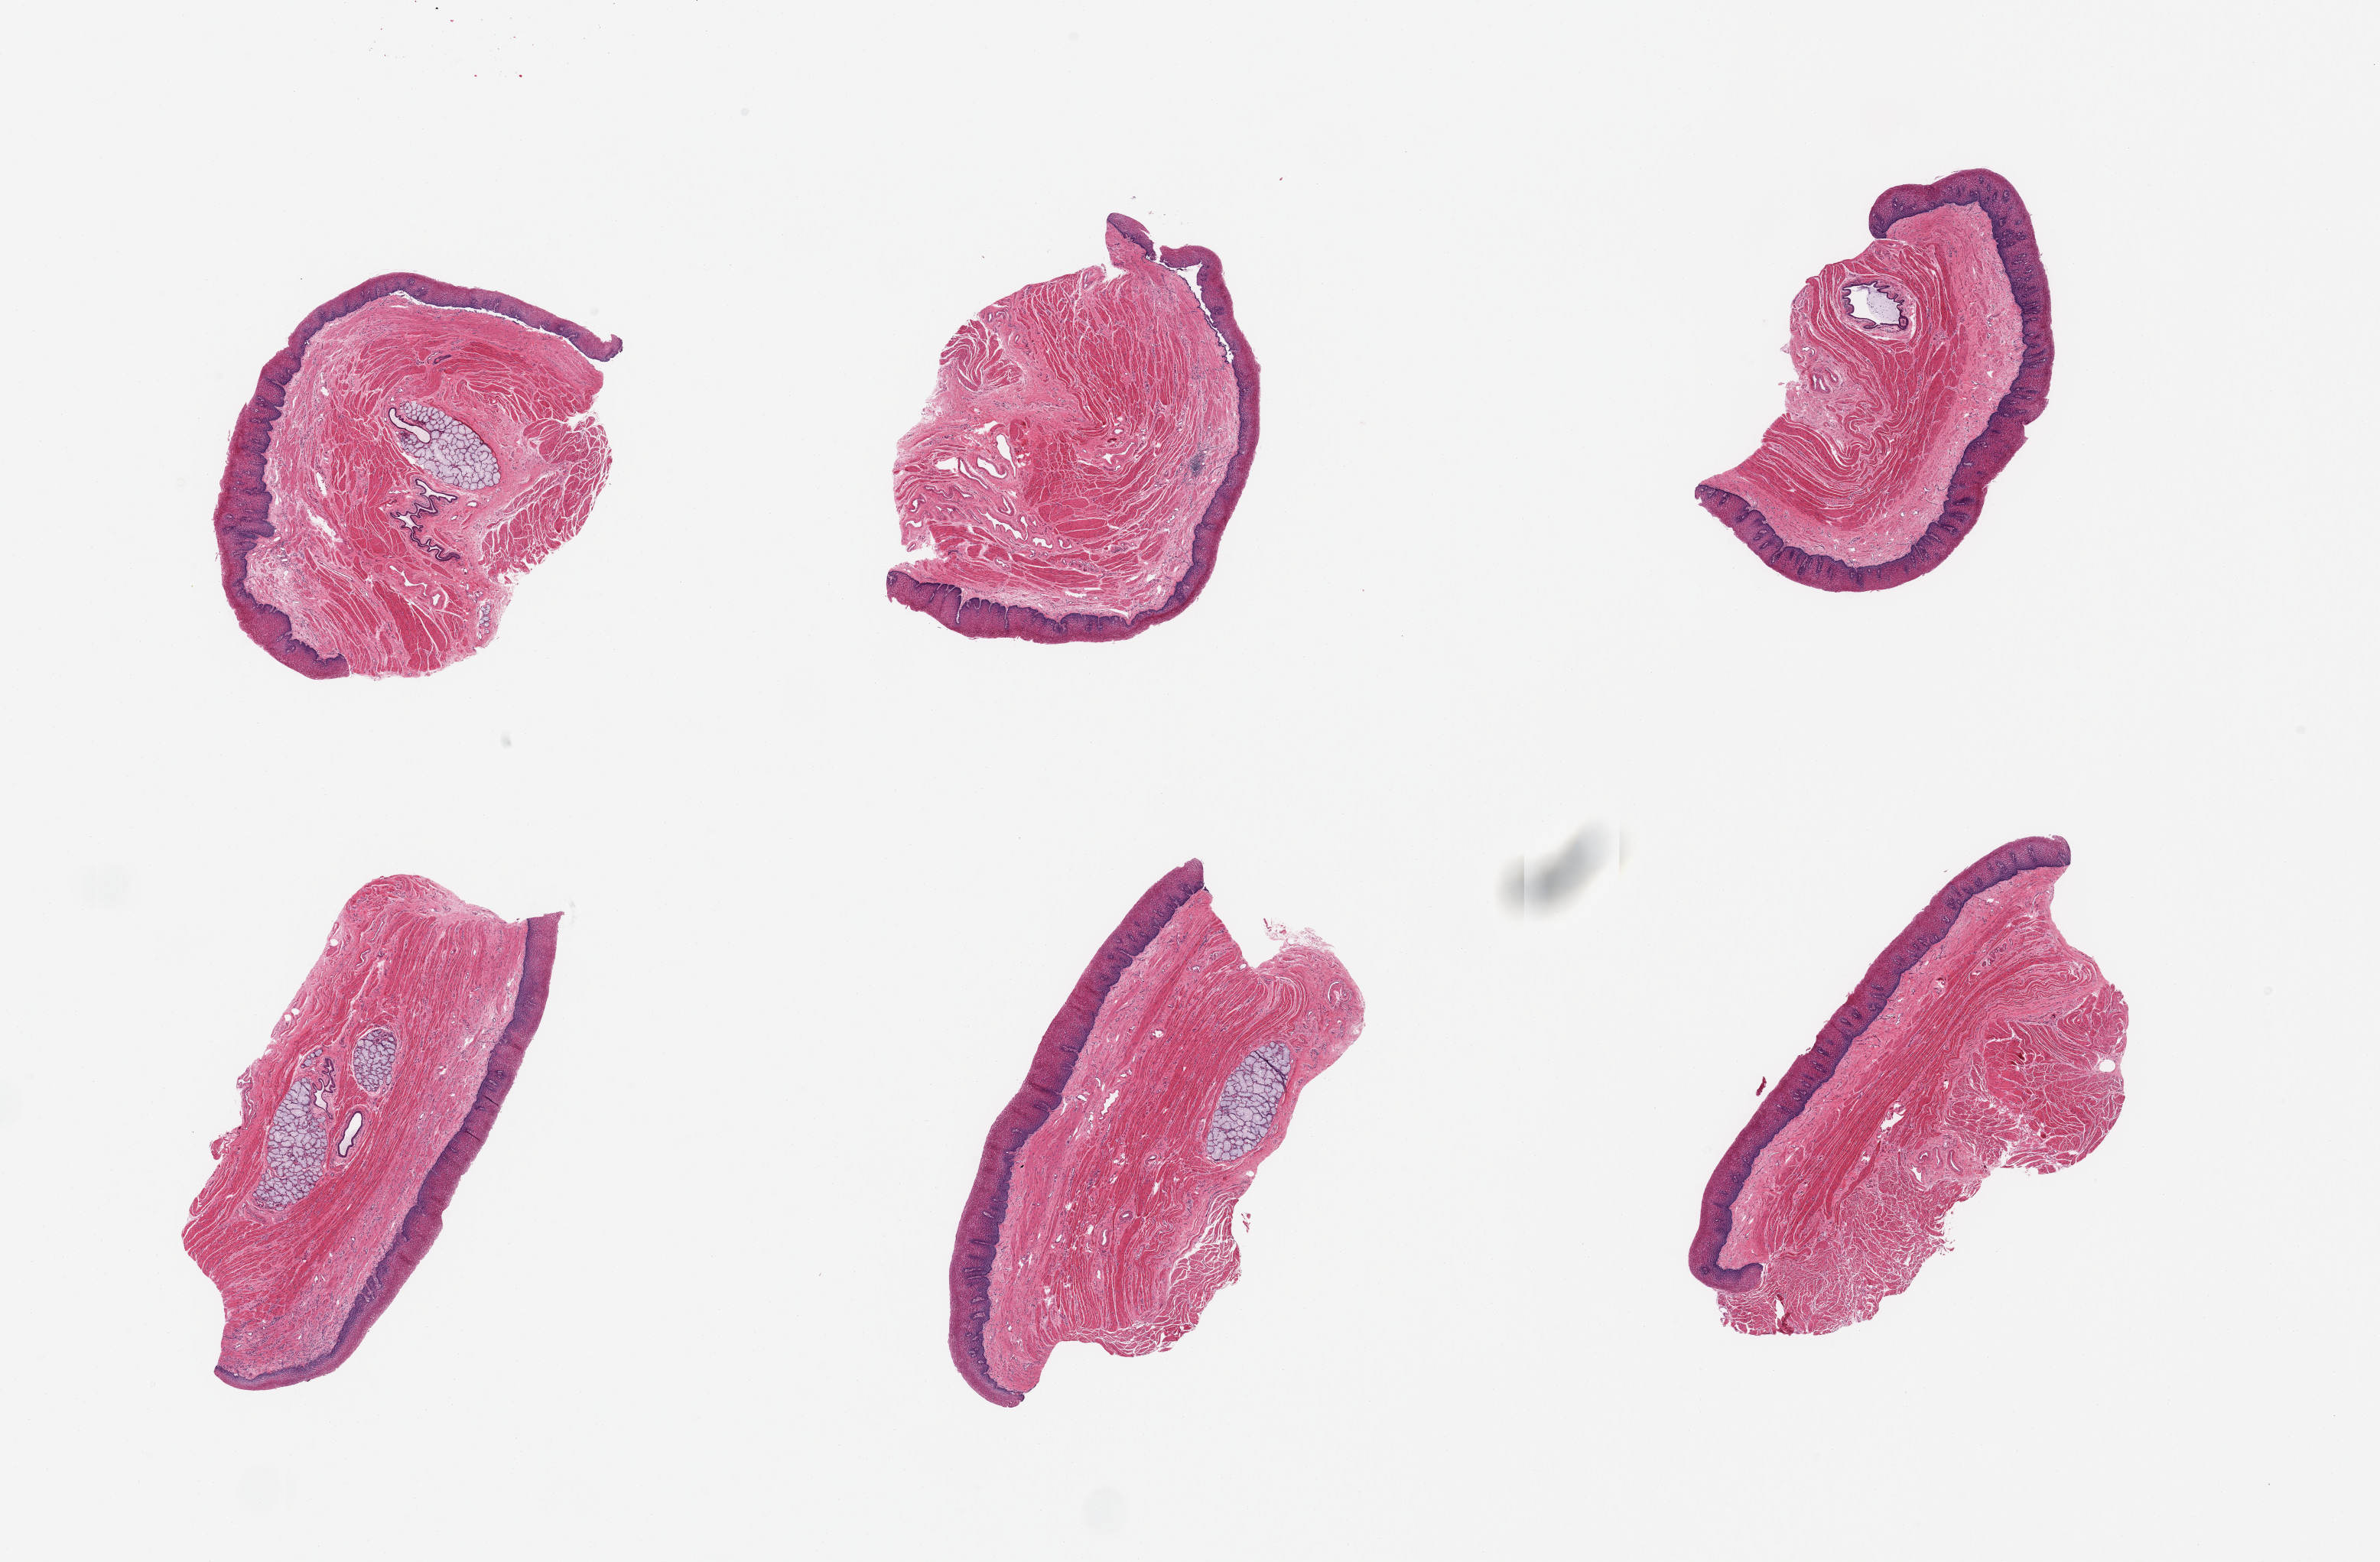
Whole-slide image, haematoxylin and eosin stain — low-resolution overview of the scanned area, about 24.6 x 16.2 mm (acquisition: 20x scan); PAXgene-fixed paraffin-embedded (PFPE) section; section of esophageal mucous membrane (target tissue); tissue donor sample. Donor sex: male.
- reviewer comment on this tissue sample: 6 pieces; squamous mucosa & submucosa, not muscularis propria (esophagus-mucosa)